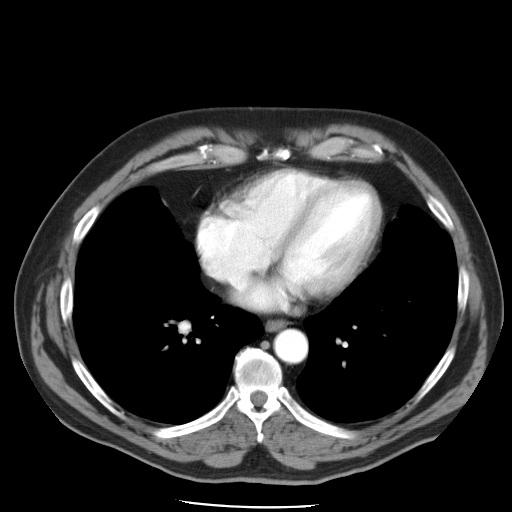
Contrast-enhanced abdominal CT, one axial slice; position 49 of 49 along the scan axis; reconstruction kernel STANDARD; soft-tissue window (W 400 / L 40 HU); 512 × 512 image matrix. Male patient, age 68 years. Case-level facts recorded for this patient, not image findings: diagnosis: colorectal cancer liver metastases, imaged before liver resection; multiple liver metastases: yes; largest metastasis: 1.7 cm; disease in both lobes: no.
Outlined on this slice (outlined manually by an expert reader):
- hepatic veins: box from (x=223, y=280) to (x=250, y=293) px